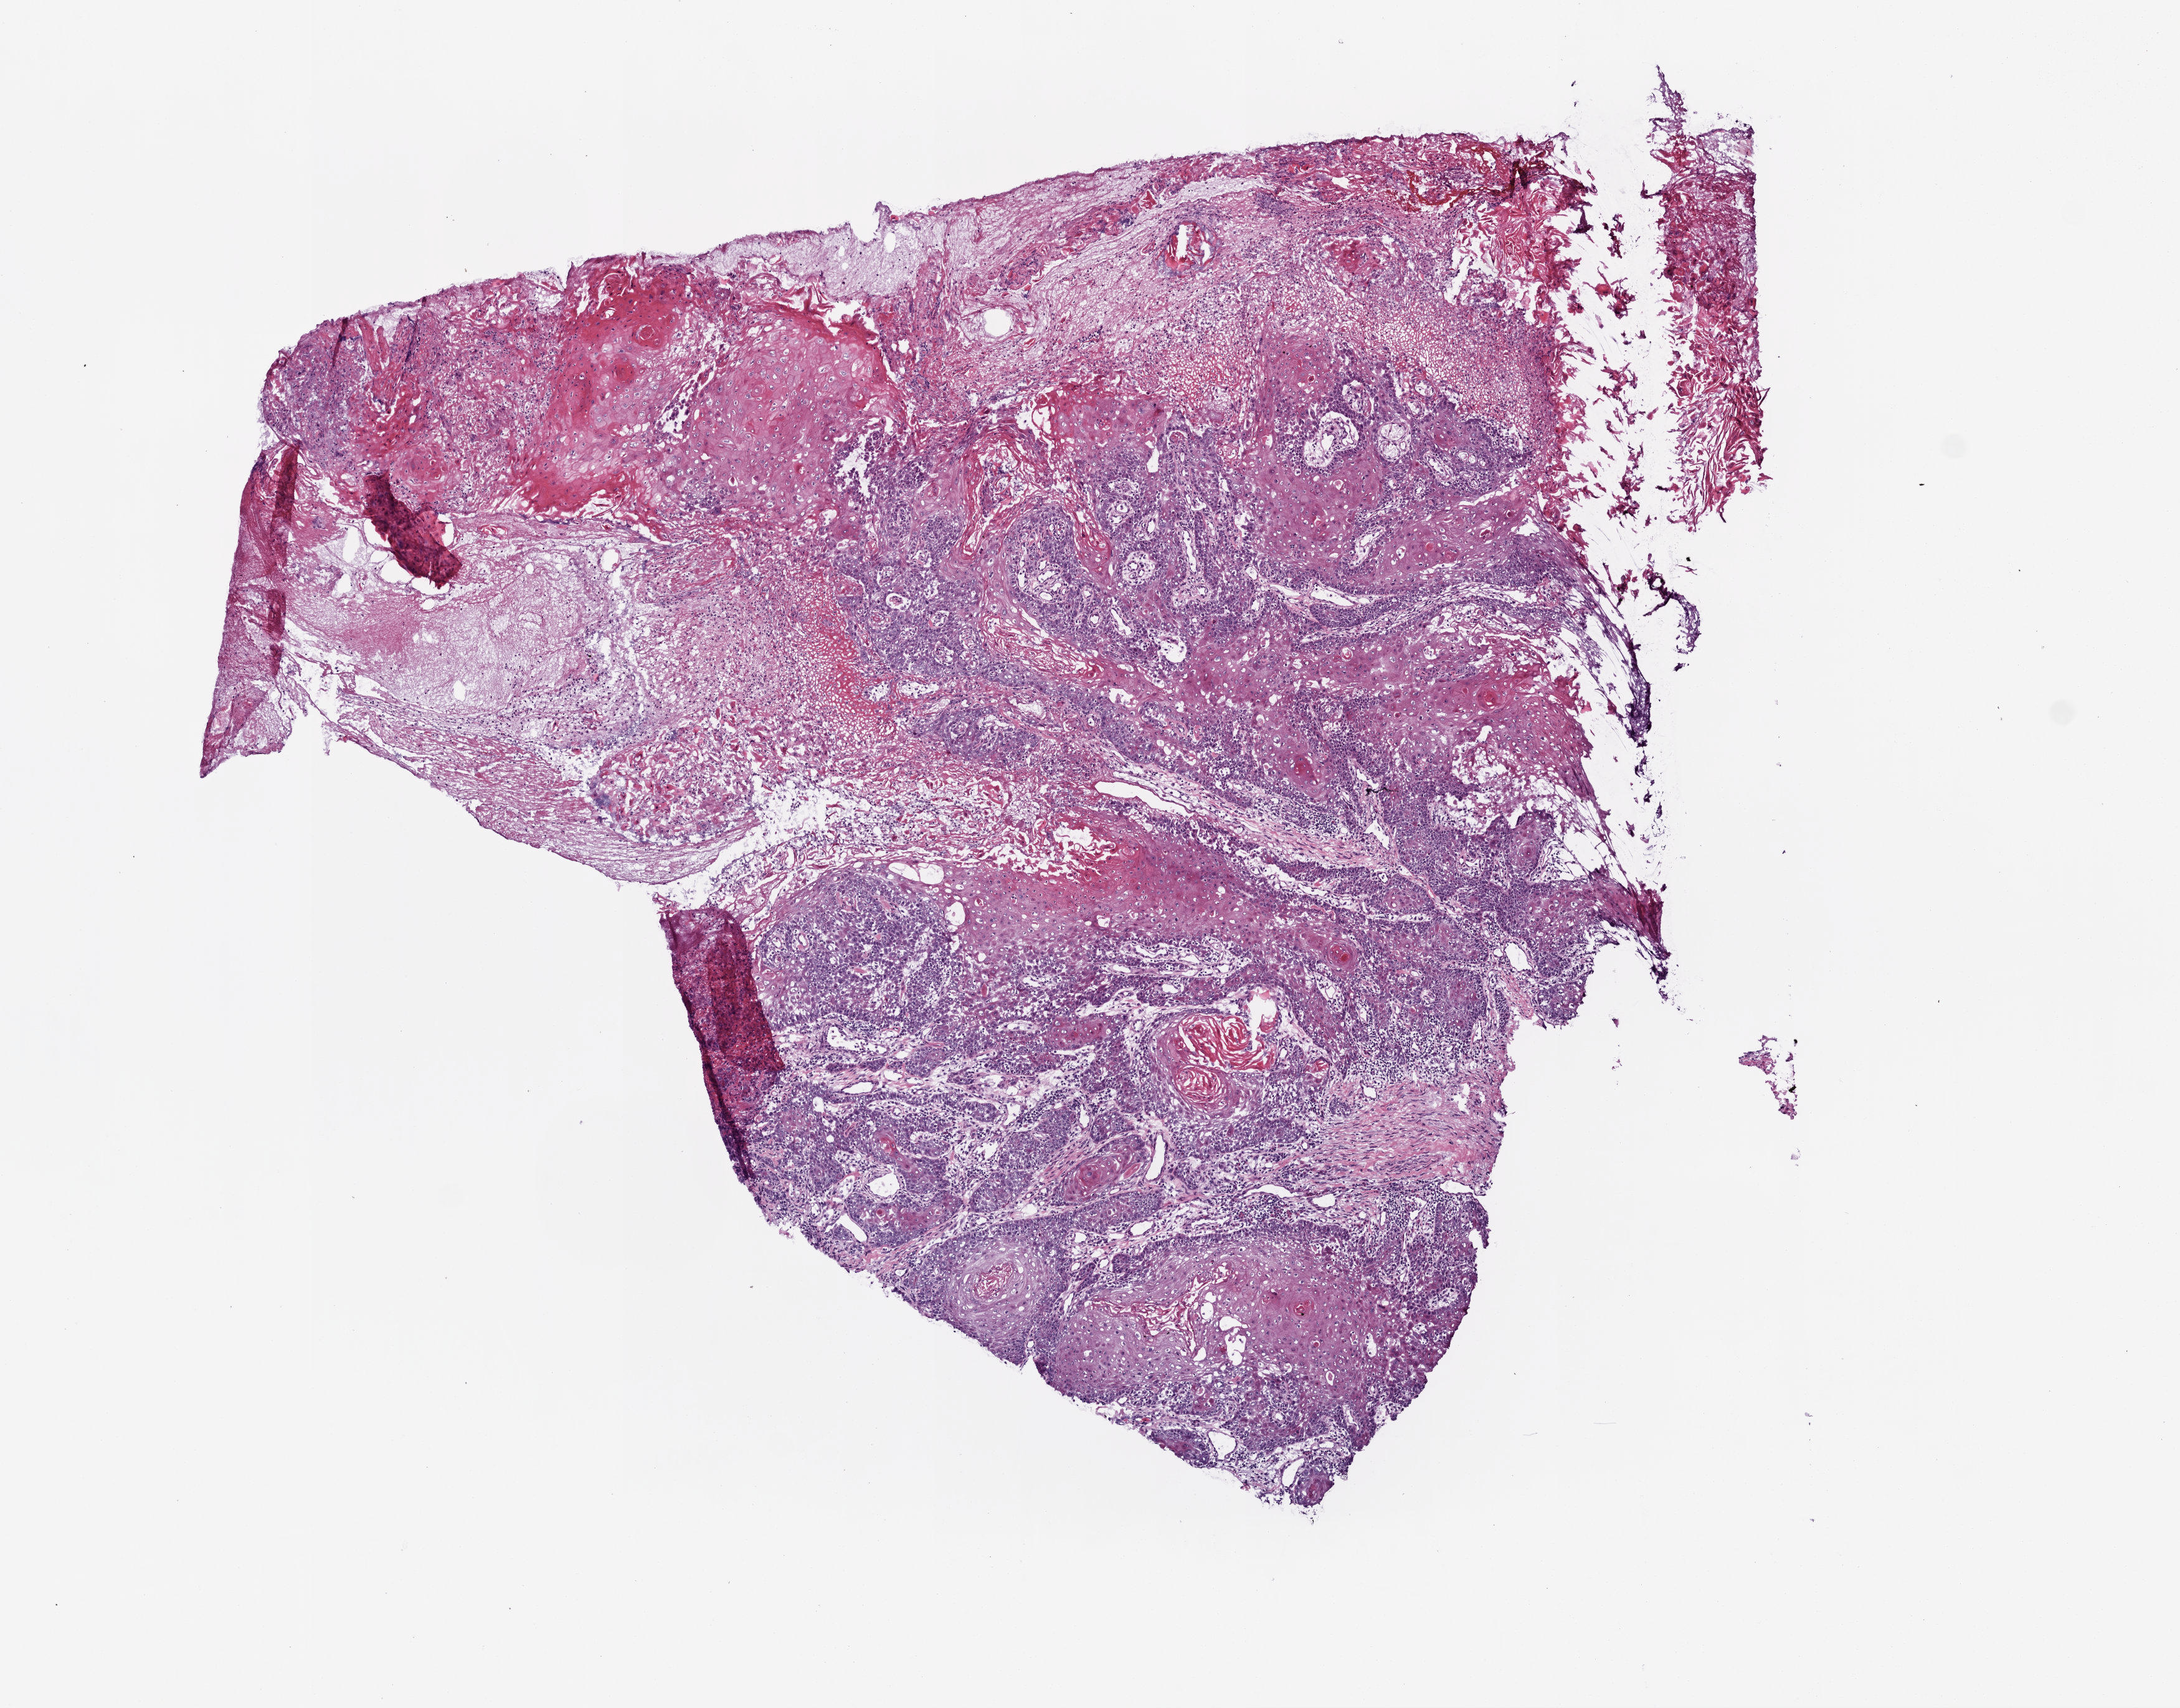
H&E-stained whole-slide image, whole scanned area (about 7.0 x 5.5 mm, acquisition: 20x scan) shown as a low-resolution overview, frozen section, head and neck, primary tumour sample. Male, age 65 years at initial diagnosis.
Pathologic diagnosis: Squamous cell carcinoma, NOS (overlapping lesion of lip, oral cavity and pharynx).